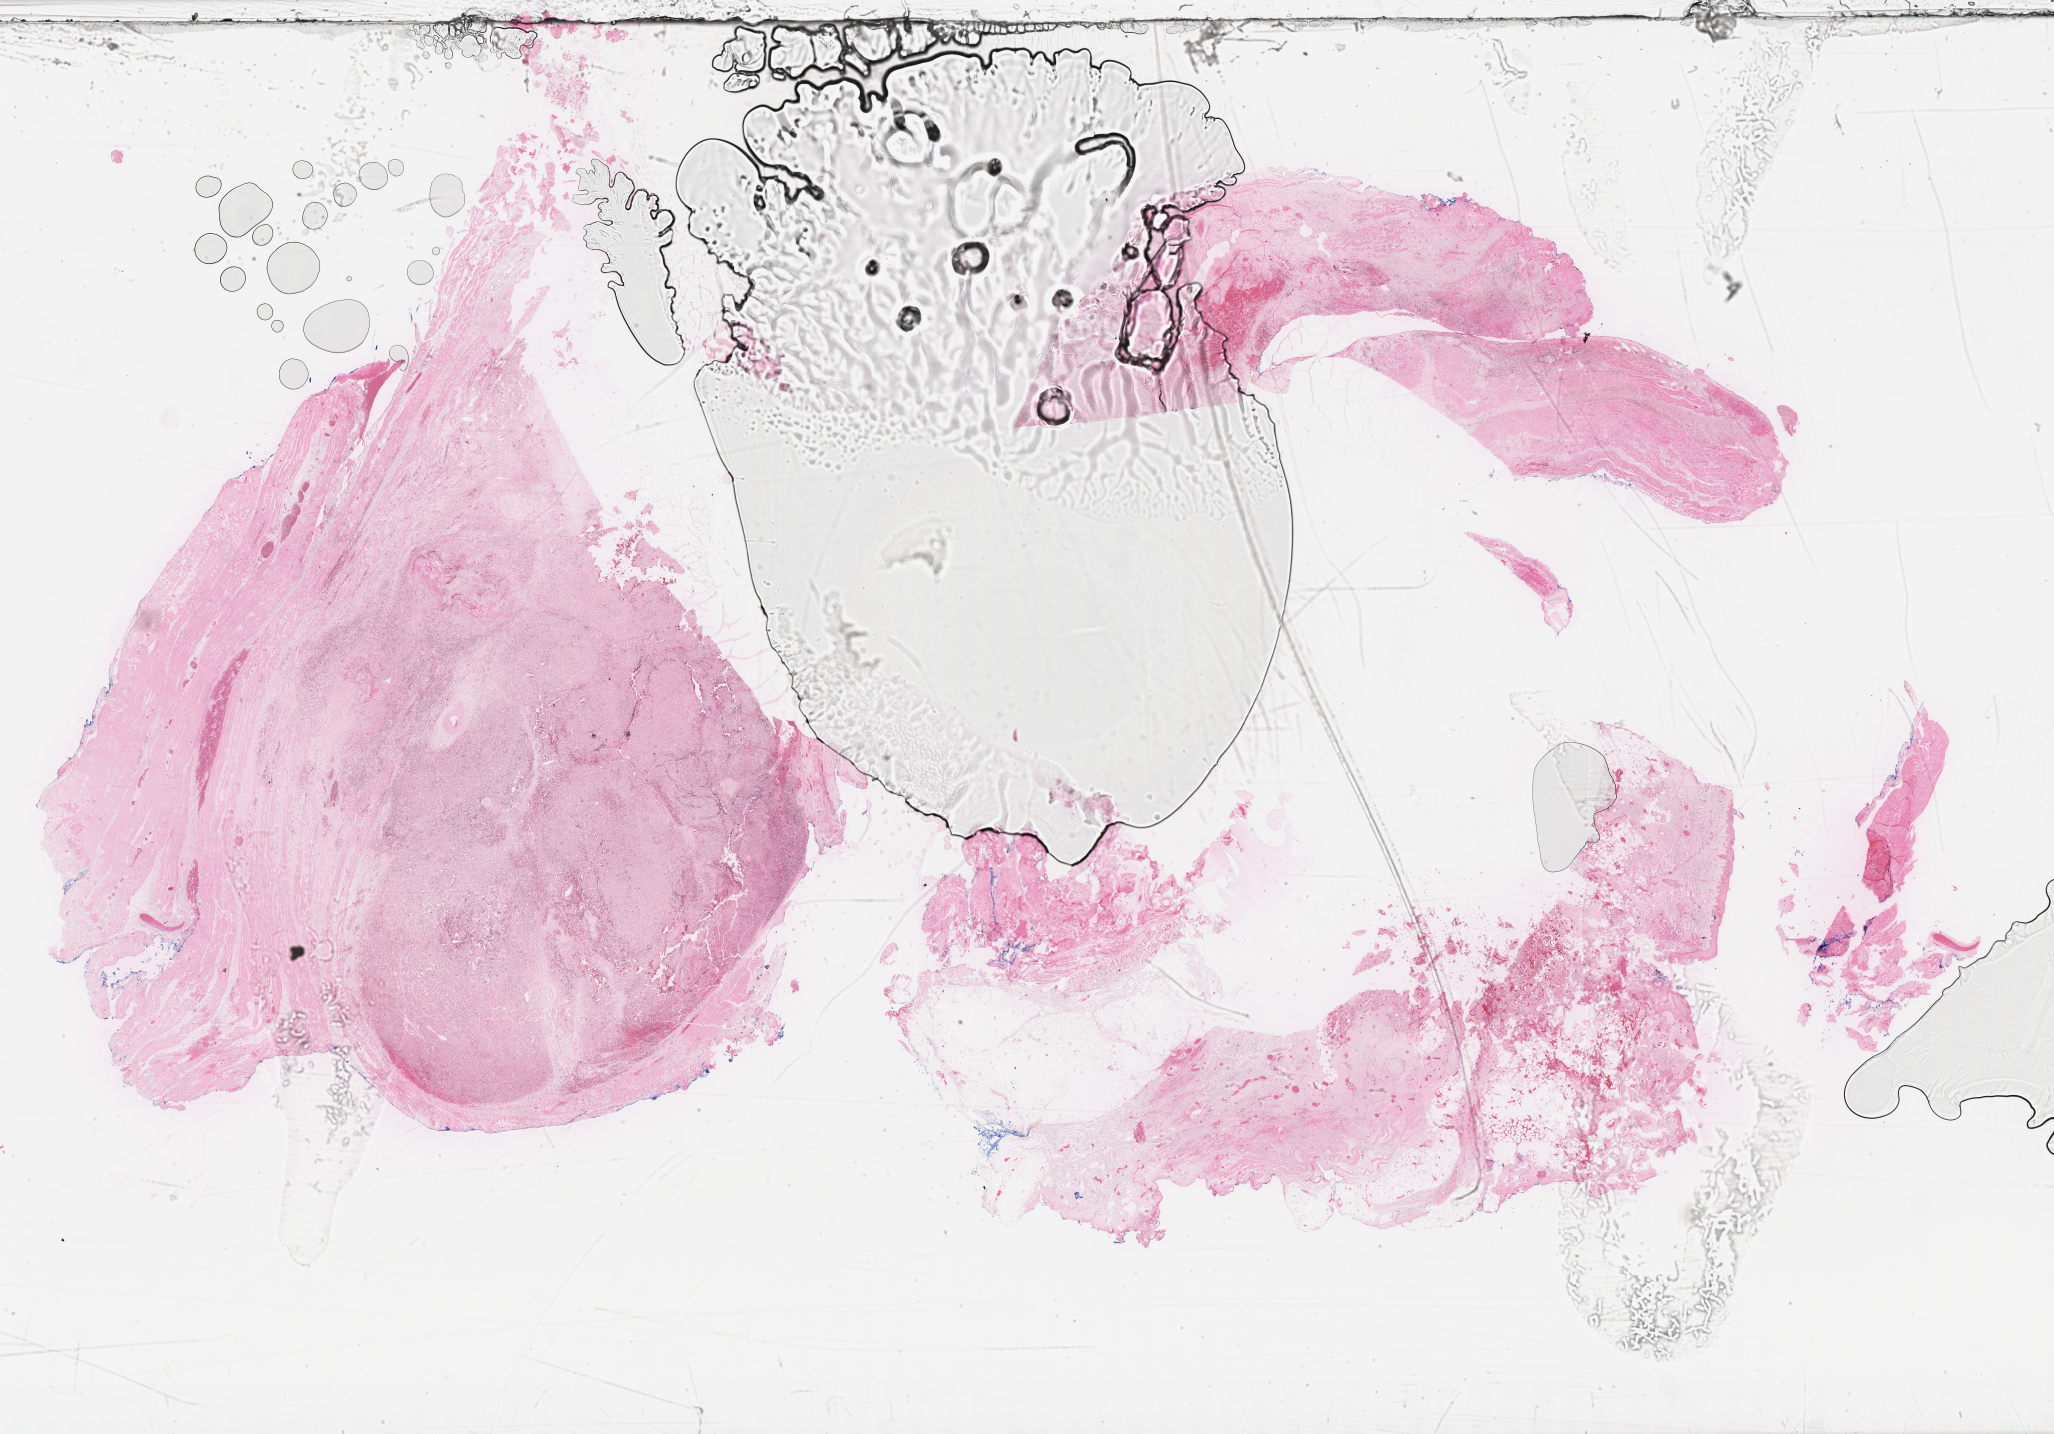
H&E whole-slide image of tumor tissue, low-resolution overview of the scanned area, about 33.2 x 23.2 mm; FFPE section; site: temple, right. Patient: female, age 6.9 years at diagnosis.
Diagnosis: rhabdomyosarcoma; histological classification: alveolar rhabdomyosarcoma.